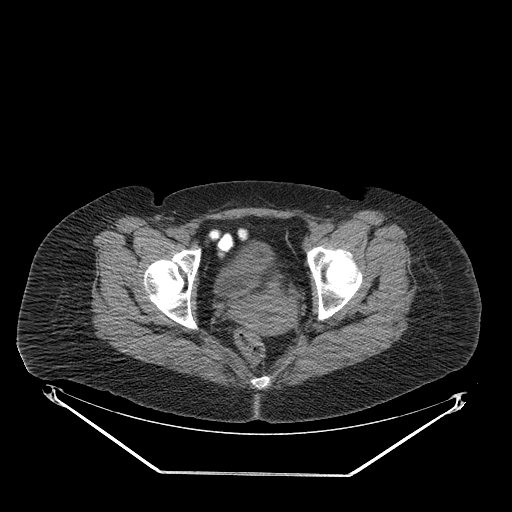
CT of an extremity soft-tissue mass (from a PET/CT study), one axial slice. Slice 63 of 267 in the series (ordered by position). Soft-tissue window (W 400 / L 40 HU). 512 × 512 image matrix, field of view 500 × 500 mm. Female patient. From the clinical record (not read from this slice): histological type: myxofibrosarcoma; grade: intermediate; site of the primary tumour: left thigh.
Annotated regions visible in this slice (expert contour drawn on MRI and transferred to this co-registered scan by the dataset authors):
- gross tumour volume including surrounding oedema: bounding box <310,233,325,250> (left, top, right, bottom; pixels)